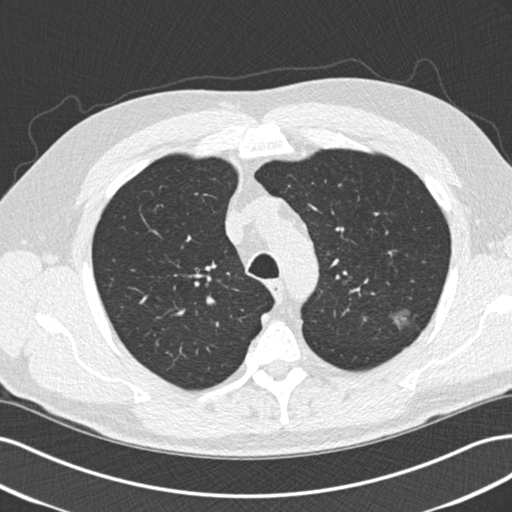
Chest CT (low-dose screening protocol), one axial image; second screening round (one year after baseline); lung window (W 1500 / L -600 HU); 2 mm slice thickness; slice 47 of 209 in the series. Male participant, aged 65 years at enrolment. Former smoker at enrolment.
Lesion marked by an expert reader, bounding box <384,303,425,347> (left, top, right, bottom; pixels). Reader record for this screening exam (exam-level; its link to the box is not recorded): non-calcified nodule or mass ≥4 mm, left upper lobe, 10 × 9 mm, poorly defined margins, mixed attenuation, pre-existing on the prior screen: yes; interval growth: no. Later outcome: lung cancer diagnosed 221 days after this screen — adenocarcinoma, NOS, left upper lobe, poorly differentiated (G3), stage IA (AJCC 6th edition), 13 mm at pathology.